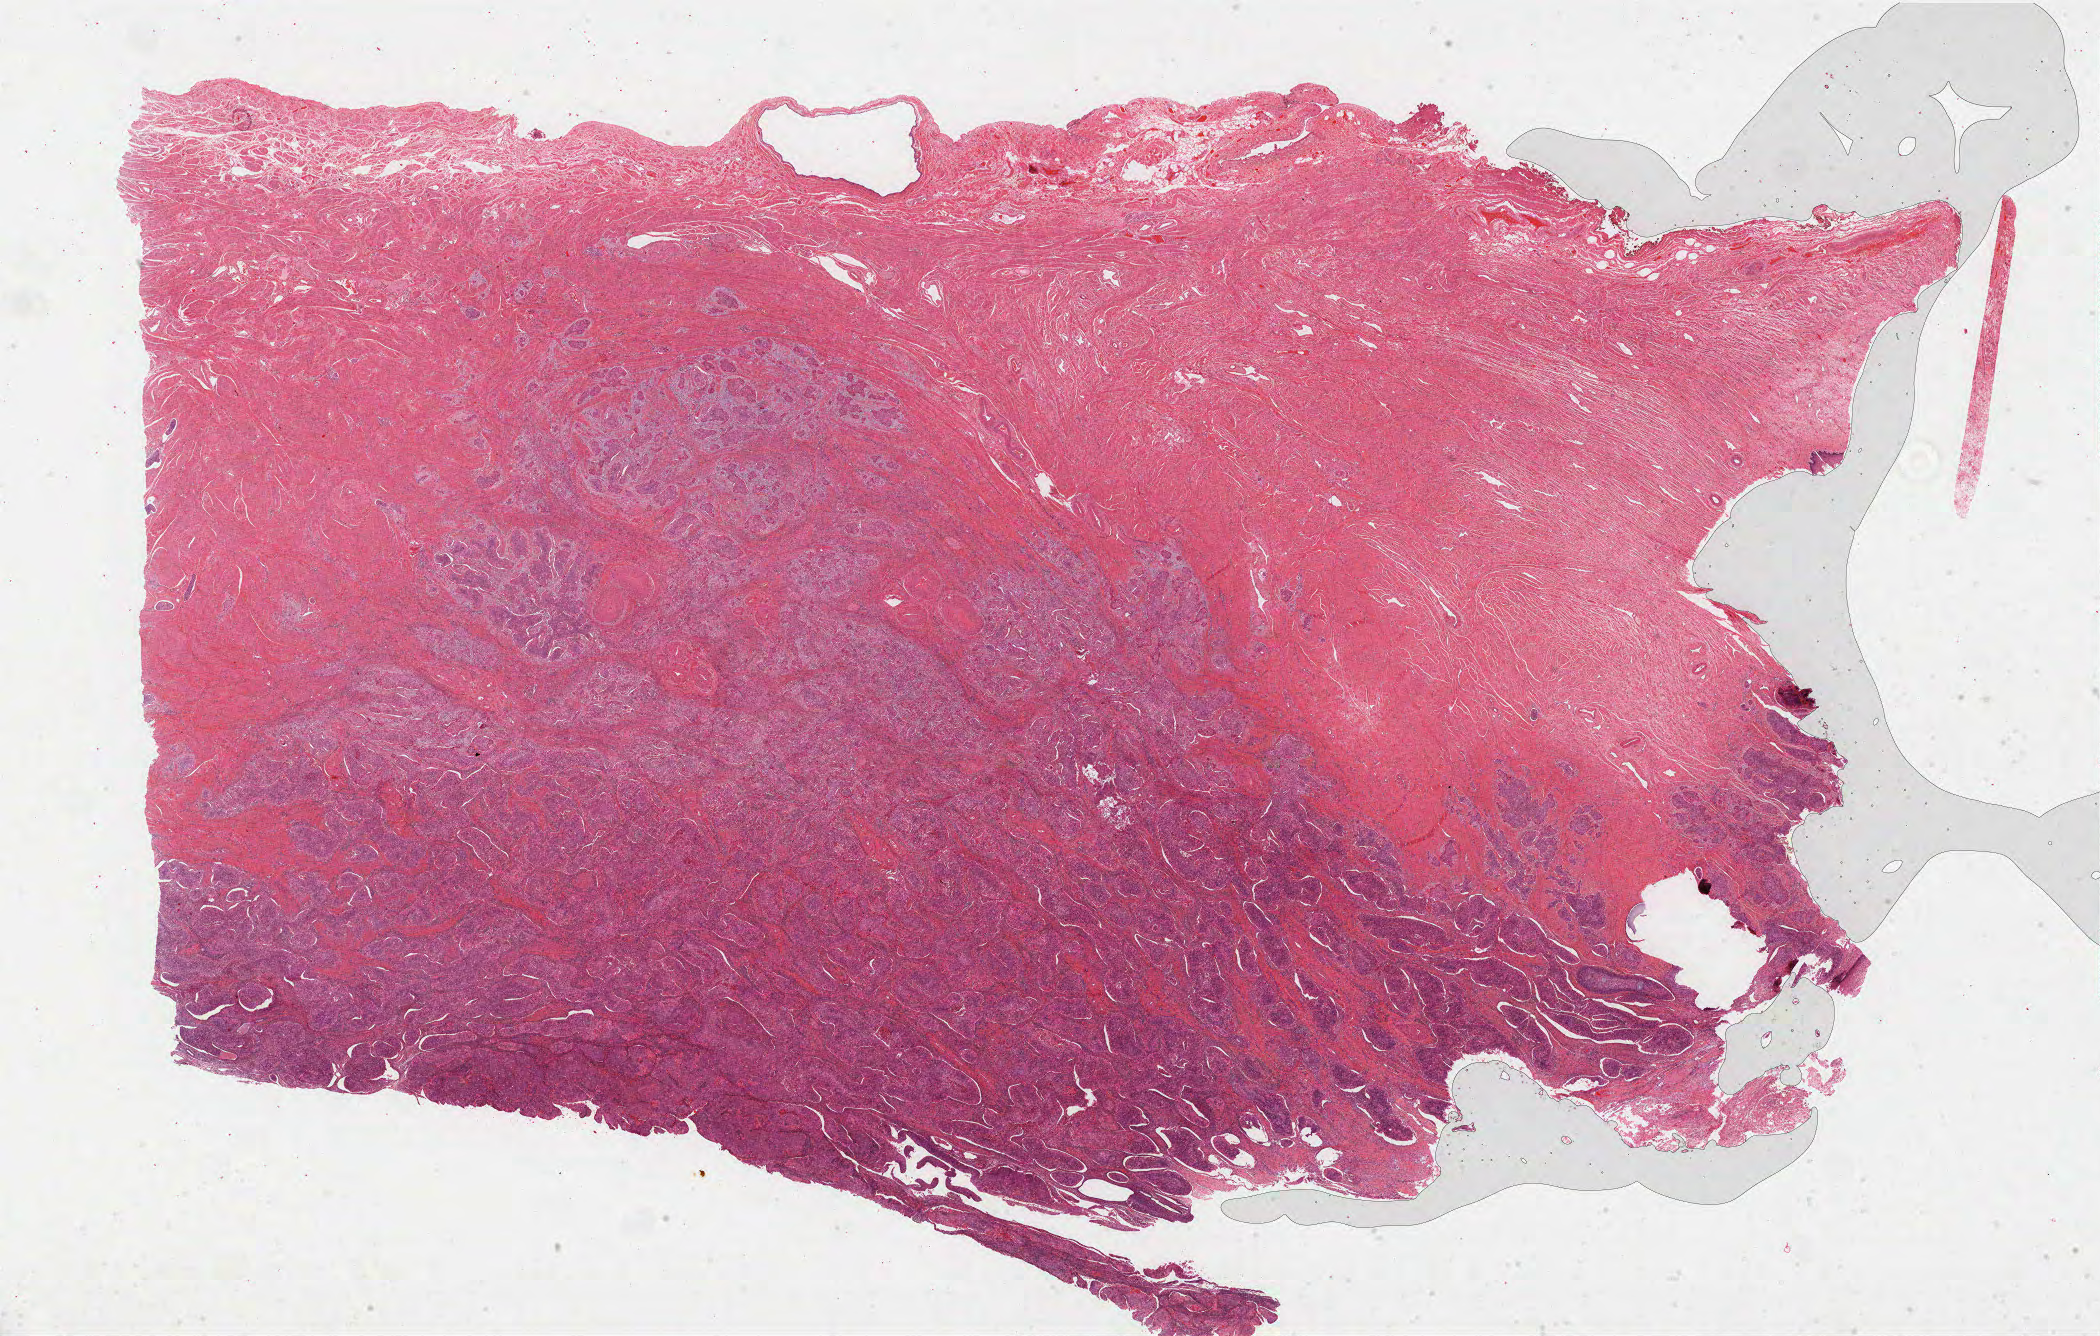
Hematoxylin and eosin (H&E) stained whole-slide image, shown as a low-resolution overview of the whole scanned area (about 33.6 x 21.4 mm), formalin-fixed paraffin-embedded (FFPE) diagnostic section, cervix, primary tumour sample. Patient: female, age at initial diagnosis 42 years. Histologic grade: G2 (moderately differentiated).
* FIGO stage: IIA
* diagnosis: Squamous cell carcinoma, keratinizing, NOS (cervix uteri)